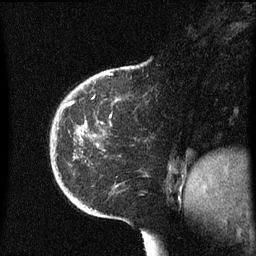
Breast MRI (dynamic contrast-enhanced), one sagittal slice; slice 15 of 60 in the series (ordered by position); dynamic contrast-enhanced series, image 2 of 3 at this slice position (ordered by acquisition); 1.5 T; TE 4.2 ms, TR 8.4 ms; 2.3 mm slice thickness; 256 × 256 image matrix. Patient: female, 38 years. Case-level facts recorded for this patient, not image findings: setting: breast cancer imaged before/during neoadjuvant chemotherapy; receptor status: HER2-positive.
Structures marked on this image (semi-automatically segmented with operator editing):
- analysis volume of interest (the breast-tissue region the enhancement analysis was run in; not a lesion): bounding box [x1, y1, x2, y2] px = [50, 78, 119, 213]
- tumour enhancement mask (voxels above the 70 % enhancement threshold inside the analysis volume of interest): [68, 102, 73, 105]